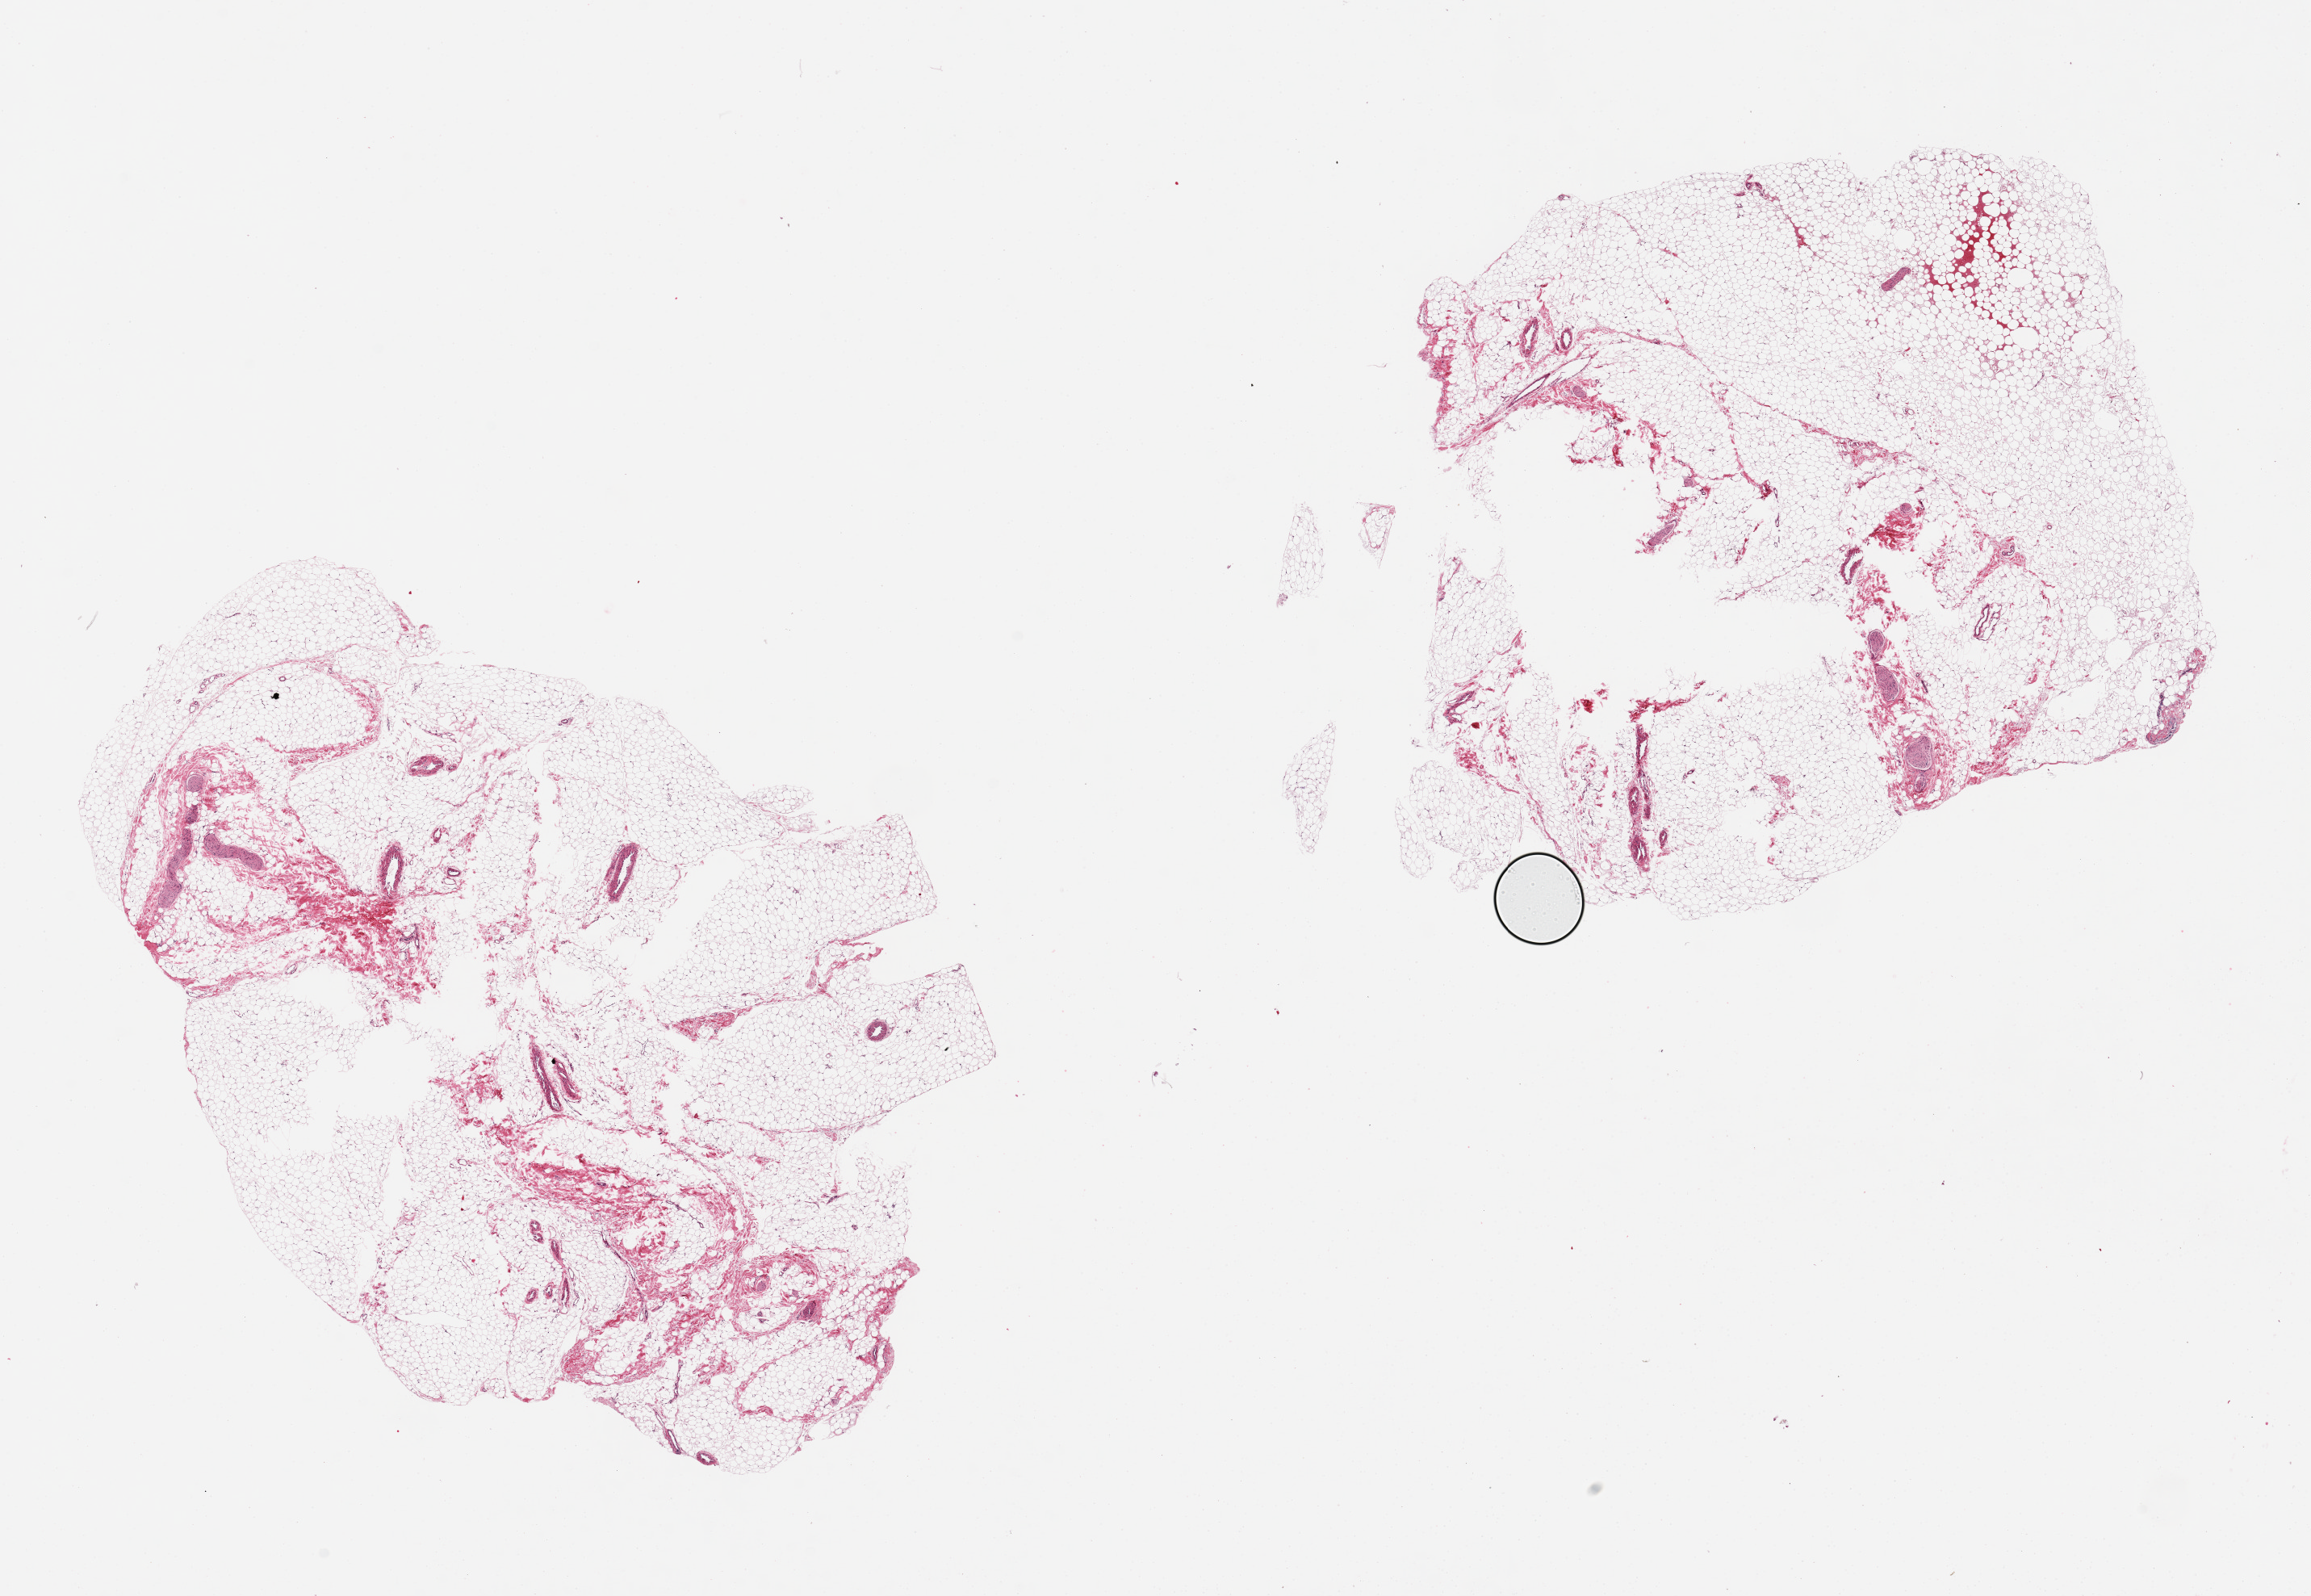
H&E whole-slide image, whole scanned area (about 22.6 x 15.6 mm) shown as a low-resolution overview; PAXgene-fixed, paraffin-embedded tissue; section of omentum (target tissue); tissue donor sample. Donor: male.
Pathologist's review note for this sample: 2 pieces, both have central defects (poor fixation), ~10% fibroconnective tissue, vessels, and nerve in both.